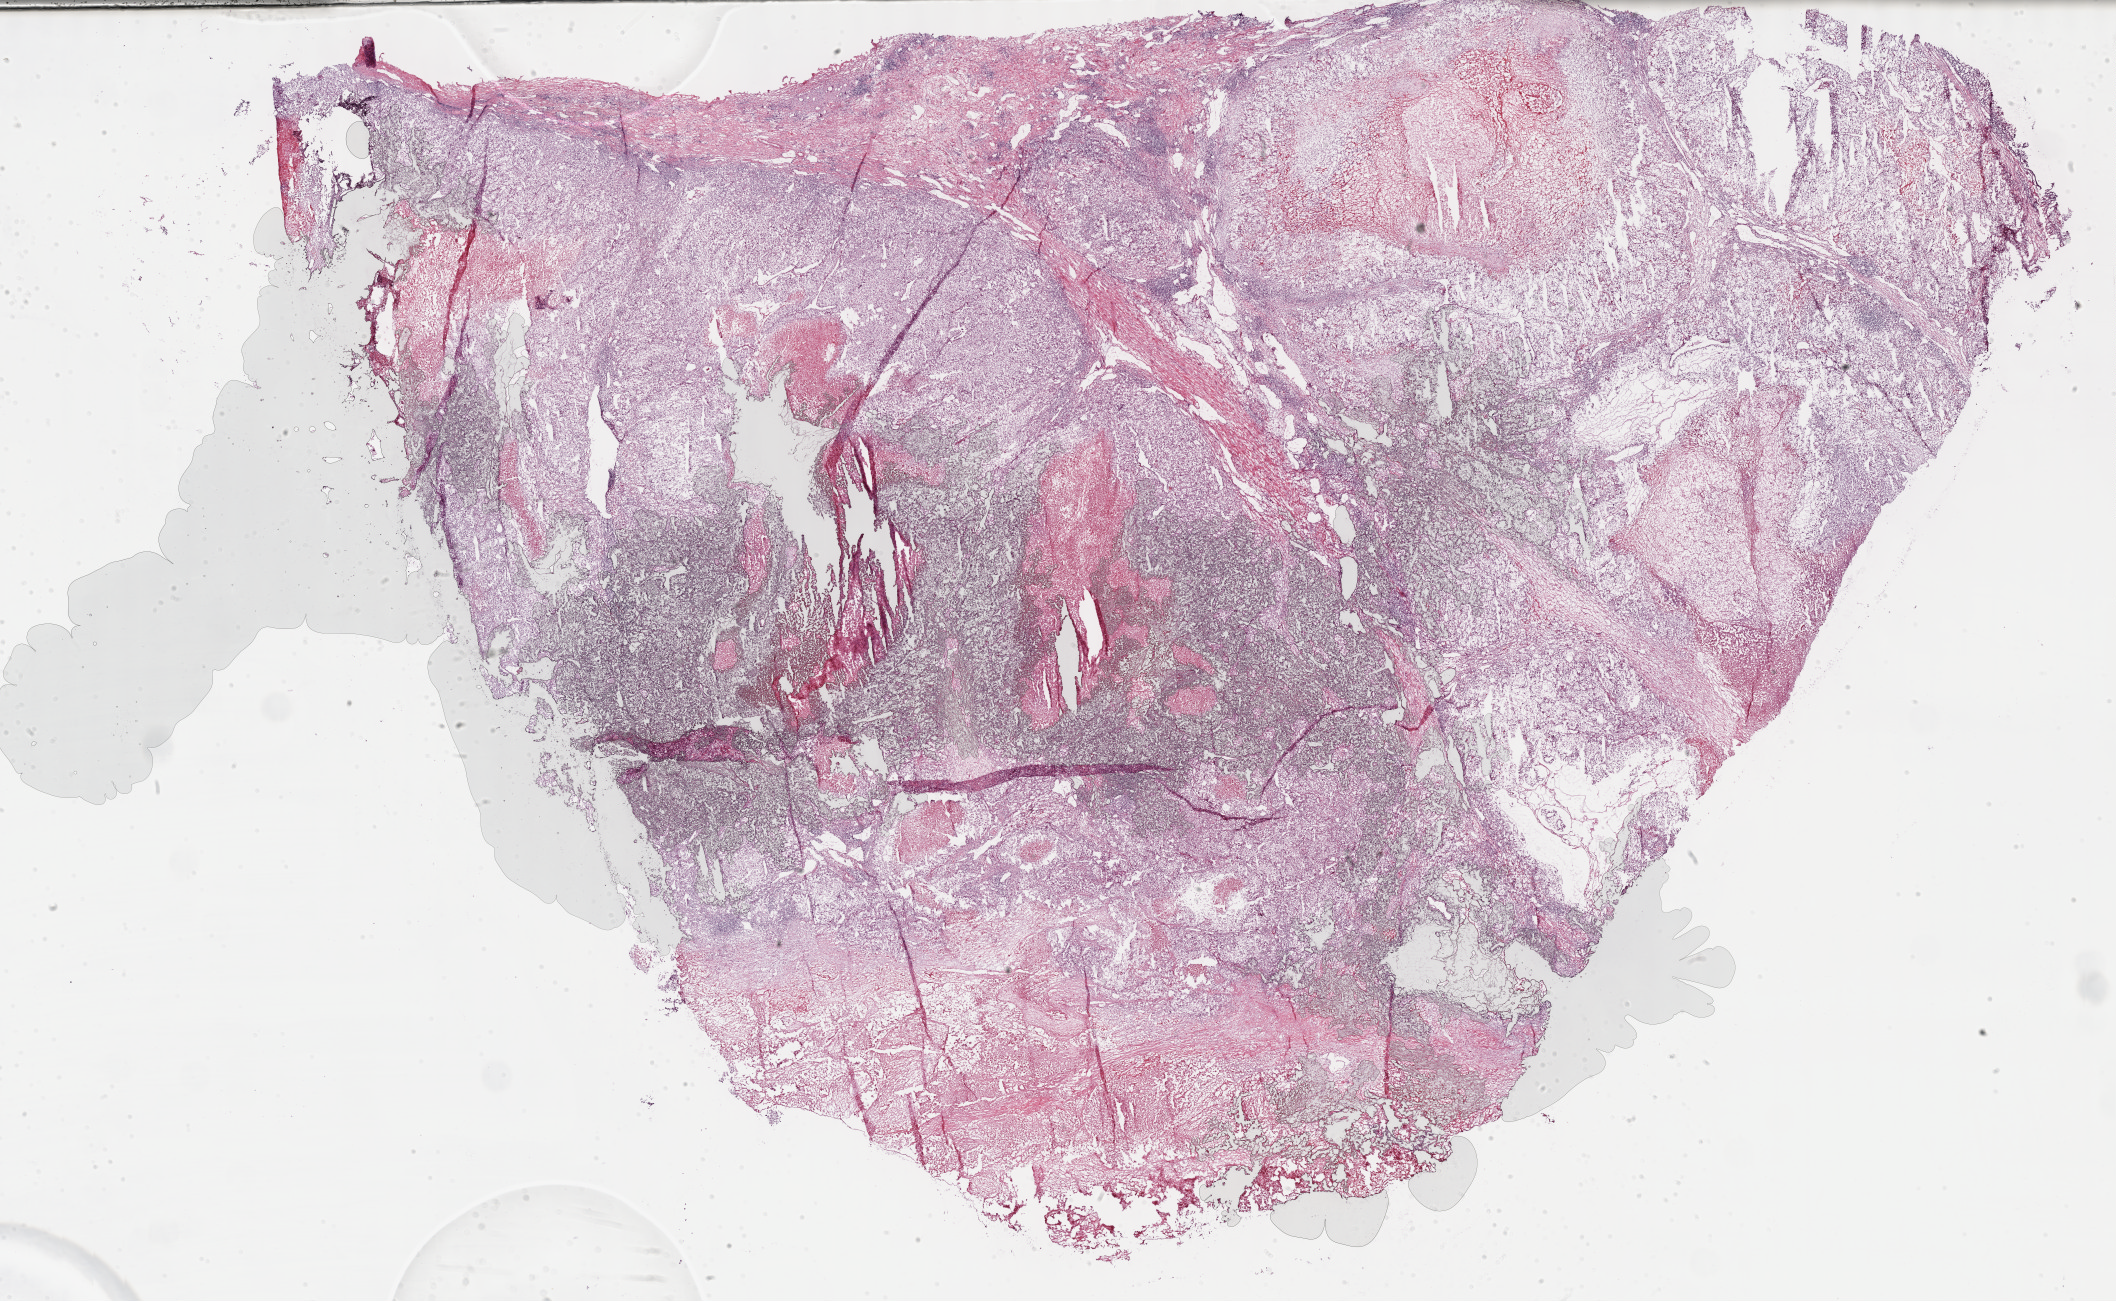
Whole-slide histology image, H&E-stained — shown as a low-resolution overview of the whole scanned area (about 34.2 x 21.0 mm, acquisition: 40x scan), frozen section, primary tumour sample from the kidney. Male, age 60 years at initial diagnosis. Histologic grade: G4 (undifferentiated). Pathologist review of this section (percent, as recorded): tumour cells 60%, tumour nuclei 70%, normal cells 0%, stromal cells 15%, necrosis 25%.
- diagnosis: Clear cell adenocarcinoma, NOS
- AJCC pathologic stage: IV (6th edition)